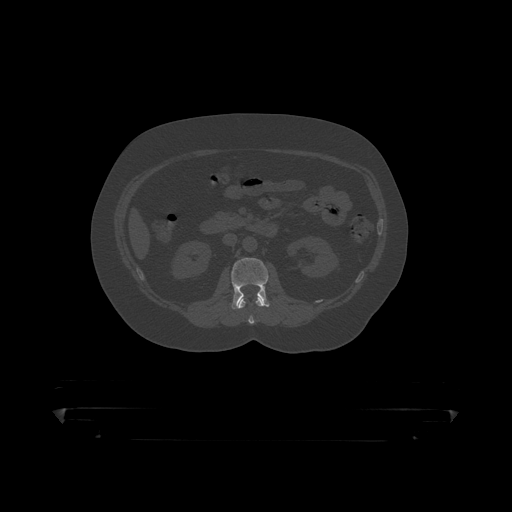
CT including the spine, one axial slice; slice 127 of 390 in the series (ordered by position); reconstruction kernel STANDARD; 120 kVp; bone window (W 1800 / L 400 HU); 1.25 mm slice thickness; 512 × 512 image matrix, field of view 650 × 650 mm. Male patient, age 60 years. Case-level facts recorded for this patient, not image findings: primary cancer: prostate.
Annotated regions visible in this slice (semi-automatically segmented with operator editing):
- L1 vertebra: bounding box (x1, y1, x2, y2) in pixels: (239, 299, 265, 319)
- L2 vertebra: (231, 258, 270, 310)